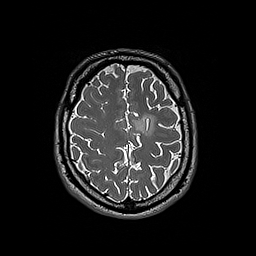
Brain MRI from a brain-tumour surgery series, one axial slice. 1 mm slice thickness. 256 × 256 image matrix. From the clinical record (not read from this slice): histopathology: Oligodendroglioma; WHO grade: 3; IDH mutation: yes.
Annotated regions visible in this slice (outlined manually by an expert reader):
- tumour: bounding box <133,114,157,136> (left, top, right, bottom; pixels)